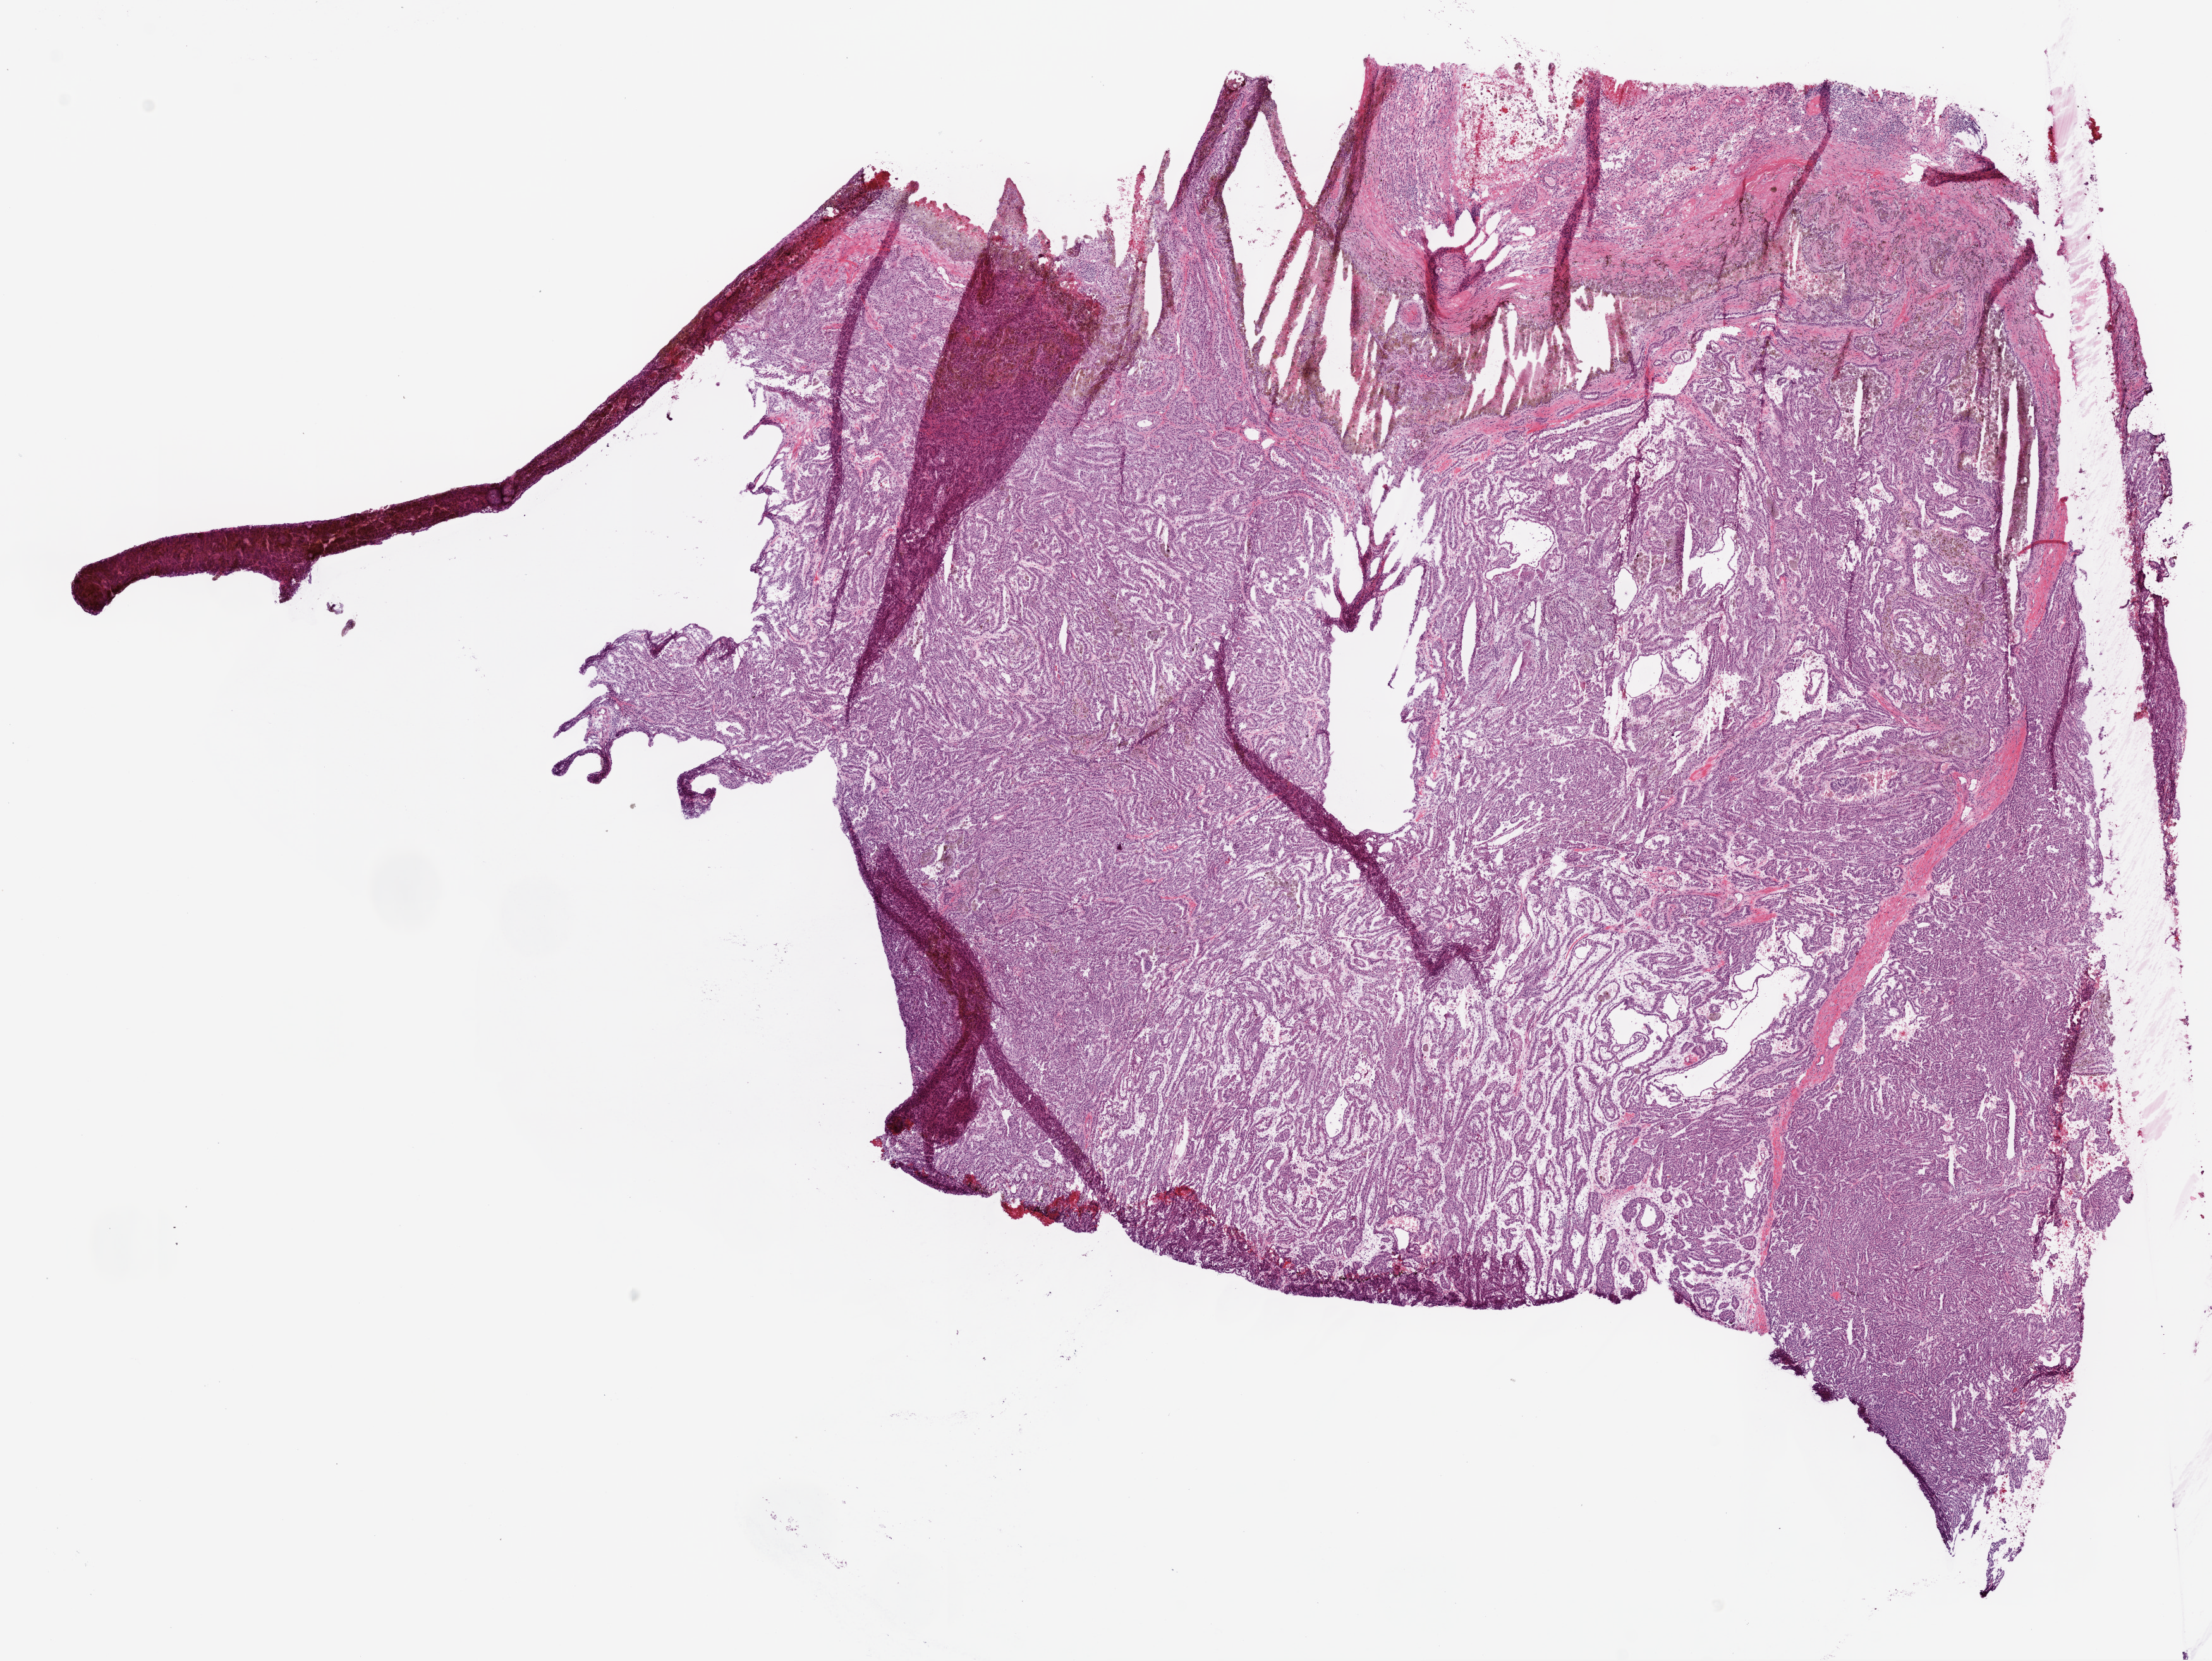
Whole-slide histology image, Hematoxylin and eosin (H&E) stained, whole scanned area (about 14.0 x 10.5 mm, from a 20x scan) shown as a low-resolution overview; frozen section; sample: primary tumour, kidney. Male, age 56 years at initial diagnosis. Slide review estimates, as recorded: tumour cells 80%, tumour nuclei 80%, normal cells 5%, stromal cells 10%, necrosis 5%.
* AJCC pathologic stage: I
* TNM: T1a NX M0
* histologic diagnosis: Papillary adenocarcinoma, NOS
* laterality: right